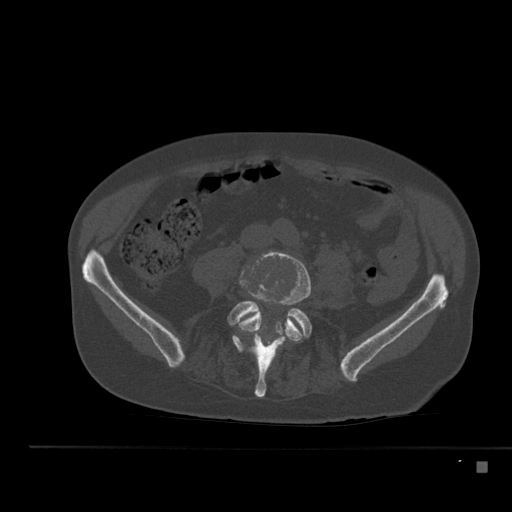
CT including the spine, one axial slice; slice 134 of 517 in the series (ordered by position); reconstruction kernel Br40s; 120 kVp; bone window (W 1800 / L 400 HU); 1.5 mm slice thickness; 512 × 512 image matrix. Male patient, age 70 years. Case-level facts recorded for this patient, not image findings: primary cancer: renal; vertebrae with lytic lesions (as recorded): T4, T6, T10, T12, L3, L4, L5.
Structures marked on this image (semi-automatic segmentation, software-assisted and operator-edited):
- L4 vertebra: bounding box (x1, y1, x2, y2) in pixels: (238, 251, 311, 359)
- L5 vertebra: (228, 301, 312, 398)